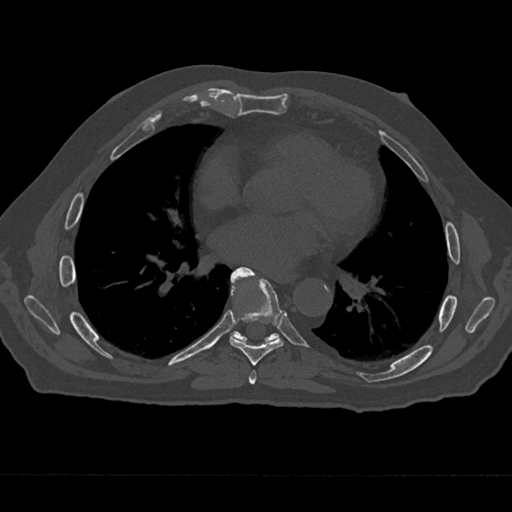
CT including the spine, one axial slice; bone window (W 1800 / L 400 HU); 0.5 mm slice thickness; 512 × 512 image matrix, field of view 377 × 377 mm. Male patient, age 75 years. Case-level facts recorded for this patient, not image findings: primary cancer: renal; vertebrae with lytic lesions (as recorded): T4.
Annotated regions visible in this slice (semi-automatic segmentation, software-assisted and operator-edited):
- T6 vertebra: bounding box (x1, y1, x2, y2) in pixels: (249, 370, 257, 385)
- T7 vertebra: (229, 267, 284, 365)
- T8 vertebra: (230, 282, 280, 342)